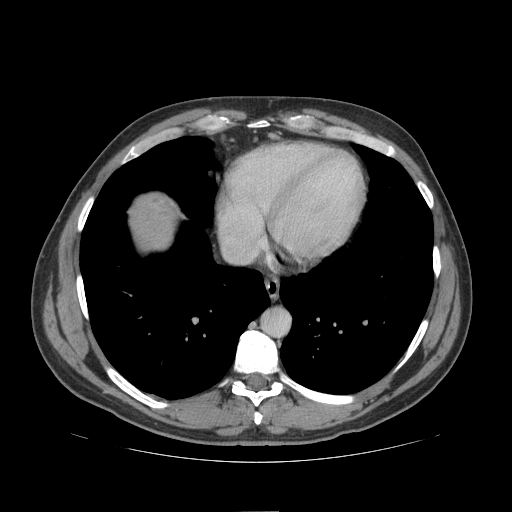
Contrast-enhanced abdominal CT (liver protocol), one axial slice. 140 kVp. Soft-tissue window (W 400 / L 40 HU). 2.5 mm slice thickness. 512 × 512 image matrix, field of view 420 × 420 mm. Case-level facts recorded for this patient, not image findings: diagnosis: hepatocellular carcinoma (patient treated with transarterial chemoembolisation; whether this scan precedes or follows treatment is not stated here); TNM stage (as recorded): Stage-IIIB; Child-Pugh class: A; tumour differentiation: poorly differentiated; tumour nodularity: multinodular.
Structures marked on this image (semi-automatic segmentation, software-assisted and operator-edited):
- liver parenchyma outside the tumour (the mass and vessels are separate outlines, so this box may not span the whole liver): bounding box <130,194,174,248> (left, top, right, bottom; pixels)